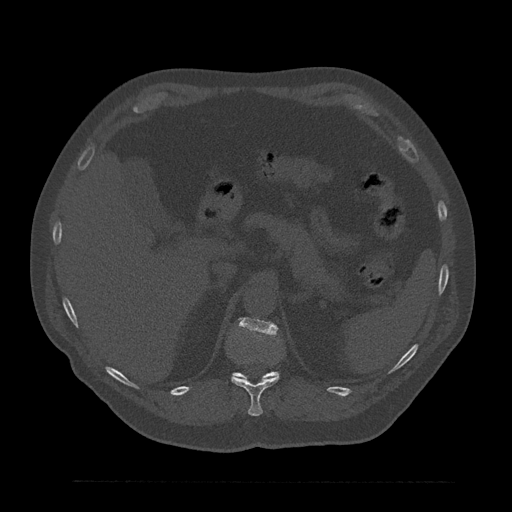
CT including the spine, one axial slice. Bone window (W 1800 / L 400 HU). 0.5 mm slice thickness. 512 × 512 image matrix, field of view 430 × 430 mm. Patient: male, 61 years. Case-level facts recorded for this patient, not image findings: primary cancer: prostate.
Structures marked on this image (semi-automatic segmentation, software-assisted and operator-edited):
- L1 vertebra: box from (x=262, y=378) to (x=267, y=380) px
- T11 vertebra: (x=231, y=359)–(x=279, y=416)
- T12 vertebra: (x=233, y=318)–(x=279, y=380)